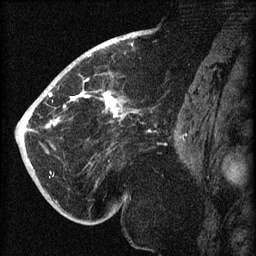
Breast MRI (dynamic contrast-enhanced), one sagittal slice. Slice 39 of 60 in the series (ordered by position). Dynamic contrast-enhanced series, image 2 of 3 at this slice position (ordered by acquisition). 1.5 T. TE 4.2 ms, TR 8.2 ms. 2 mm slice thickness. 256 × 256 image matrix, field of view 180 × 180 mm. Female patient, age 71 years.
Structures marked on this image (semi-automatic segmentation, software-assisted and operator-edited):
- analysis volume of interest (the breast-tissue region the enhancement analysis was run in; not a lesion): bounding box (x1, y1, x2, y2) in pixels: (40, 72, 142, 196)
- tumour enhancement mask (voxels above the 70 % enhancement threshold inside the analysis volume of interest): (46, 81, 120, 128)